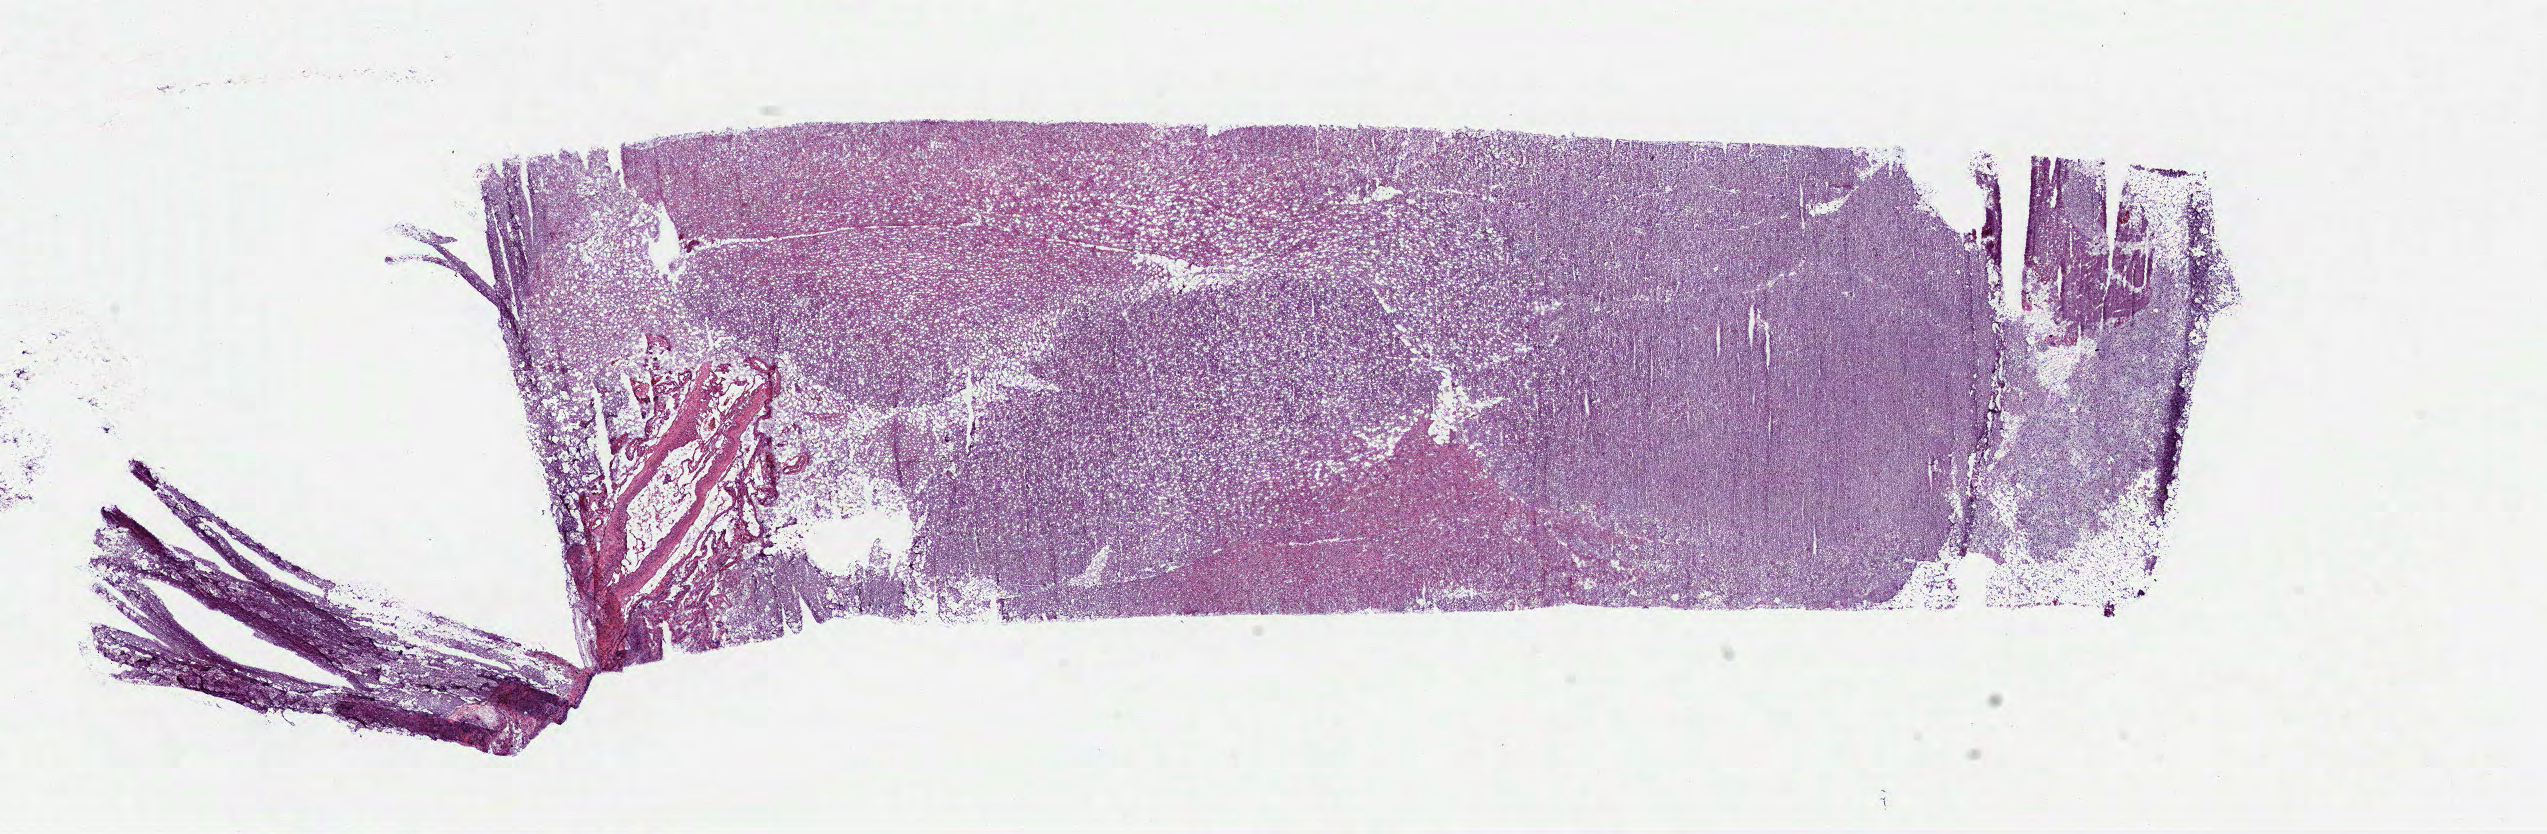
H&E-stained whole-slide image, low-resolution overview of the scanned area, about 20.5 x 6.7 mm (slide scanned at 40x), frozen section, brain, primary tumour sample. Male patient; age at initial diagnosis 35 years. Histologic grade: G3 (poorly differentiated). Composition of this section per pathologist review: tumour cells 80%, tumour nuclei 60%, normal cells 20%, stromal cells 0%, necrosis 0%.
• laterality: left
• histologic diagnosis: Oligodendroglioma, anaplastic (cerebrum)